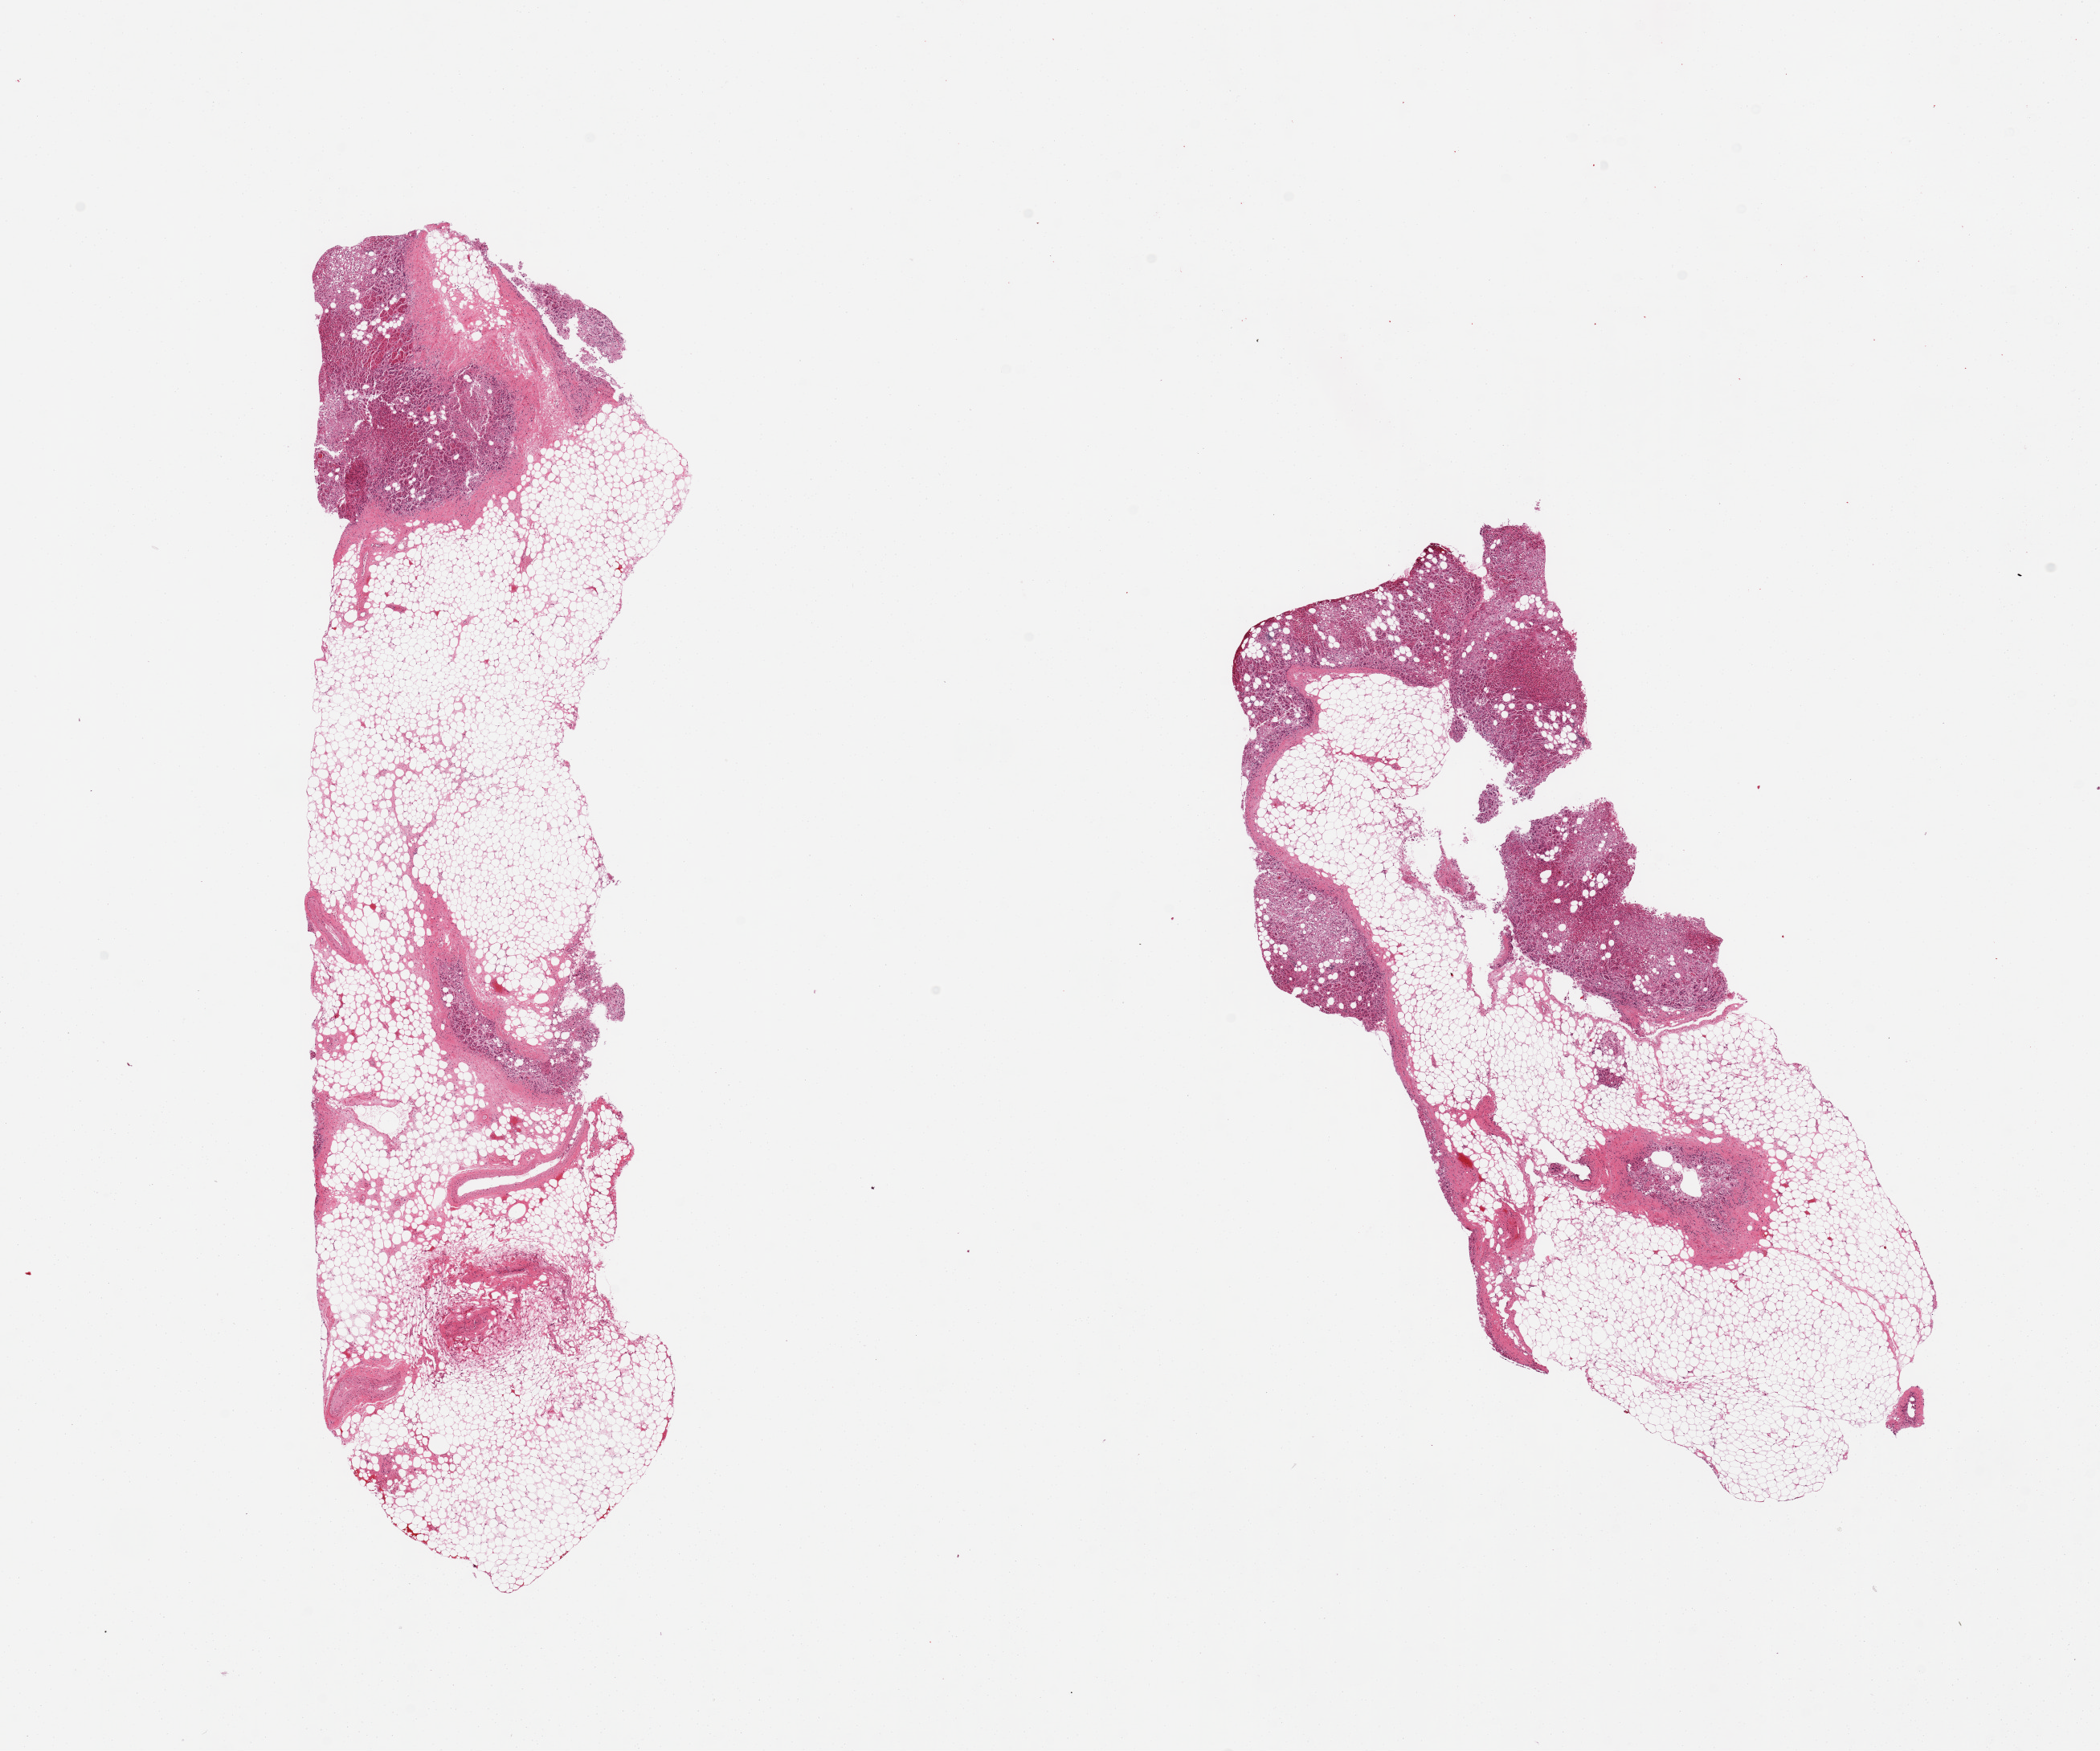
Hematoxylin and eosin (H&E) whole-slide image, brightfield, shown as a low-resolution overview of the whole scanned area (about 20.7 x 17.2 mm, acquisition: 20x scan), PAXgene-fixed, paraffin-embedded tissue, target tissue: adrenal gland, donor tissue sample.
Reviewer comment on this tissue sample: 2 pieces, predominantly fat with only 10-20% adrenal.